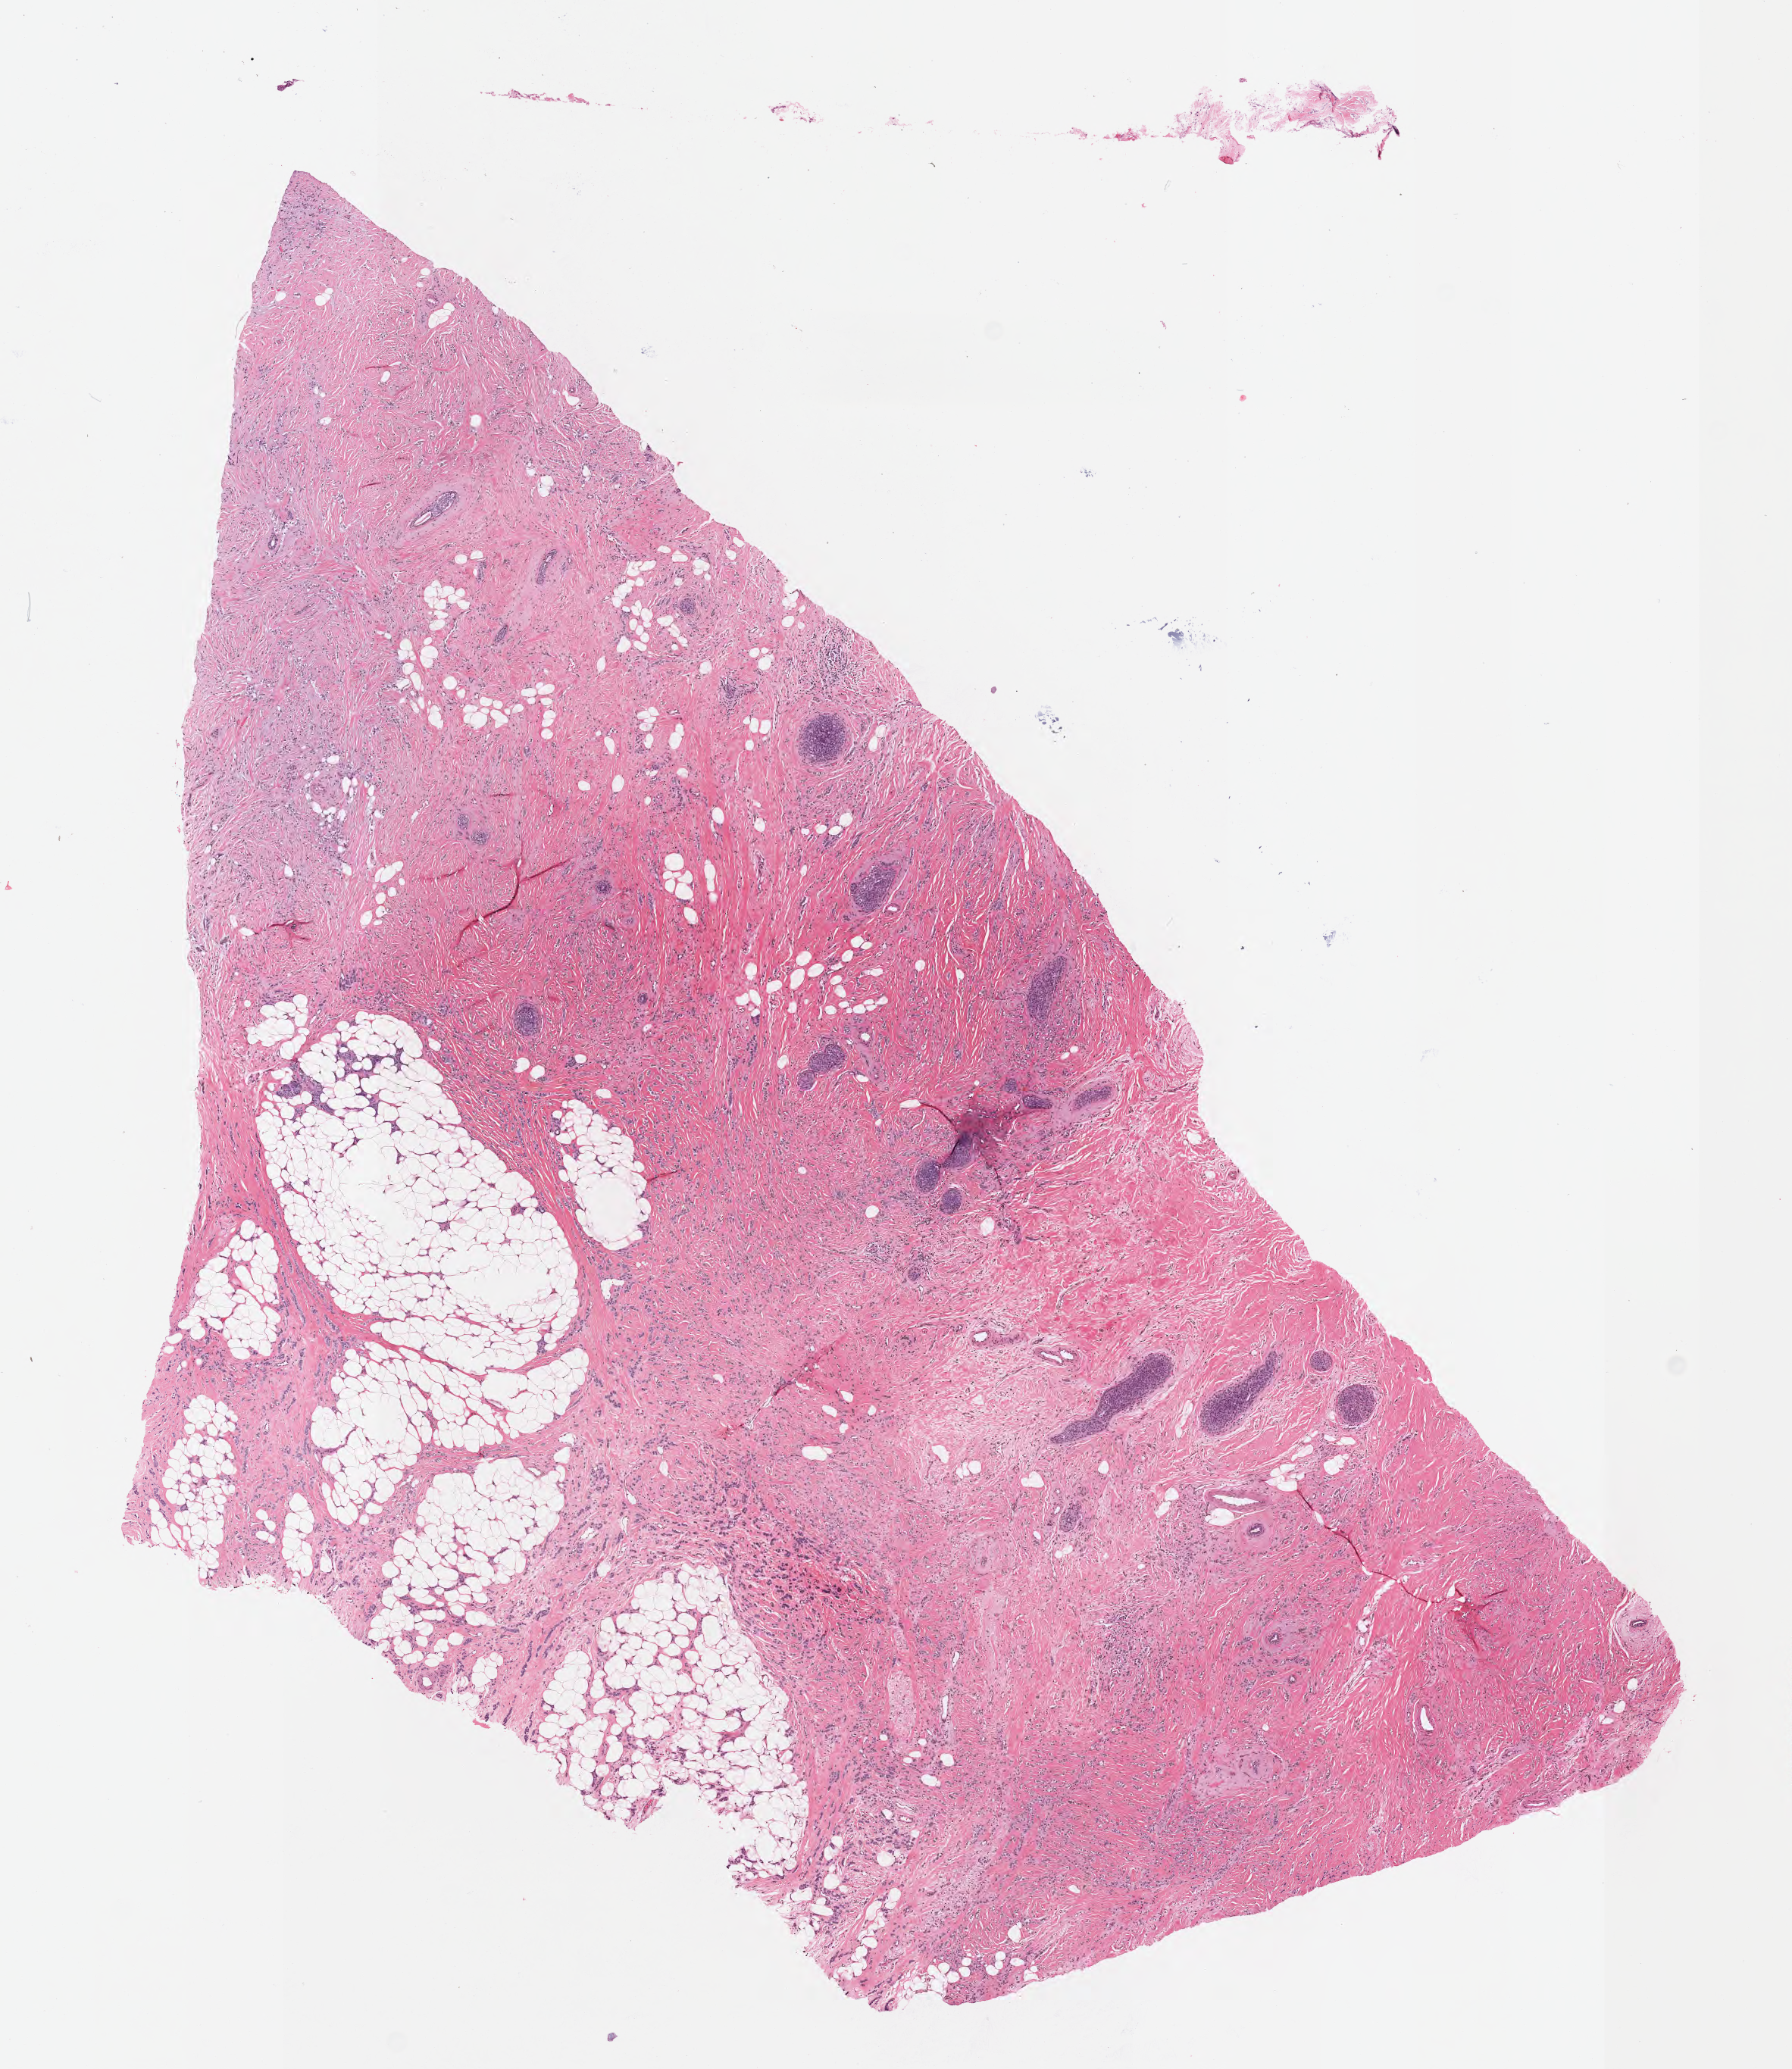
H&E whole-slide image, whole scanned area (about 9.6 x 11.0 mm) shown as a low-resolution overview; formalin-fixed paraffin-embedded section; primary tumor; anatomic site: breast. Female, age 62 years at initial diagnosis. Tumor grade: G2 (moderately differentiated). Composition of this section per pathologist review: tumor cells 80%, tumor nuclei 80%, stromal cells 16%, necrosis 0%, normal cells 4%. Inflammatory infiltration, as recorded: lymphocyte infiltration 6%, monocyte infiltration 1%, neutrophil infiltration 3%.
AJCC pathologic stage: Stage IIB. Diagnosis: Lobular carcinoma, NOS.